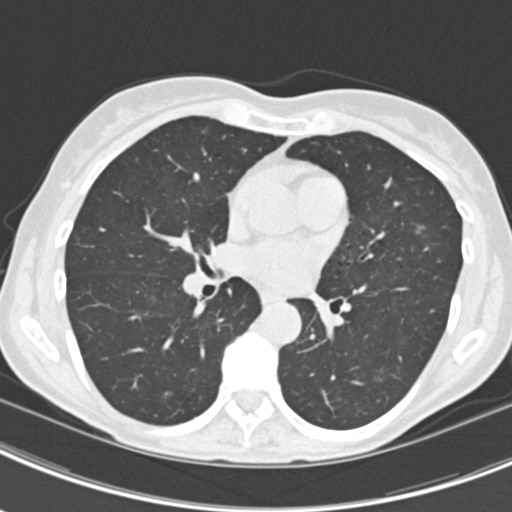
Low-dose screening chest CT, axial slice, second annual screen, lung window (W 1500 / L -600 HU), slice 96 of 219 in the series, 512 × 512 image matrix, field of view 298 × 298 mm. Female participant, aged 63 years at enrolment. Current smoker at enrolment.
Expert-annotated lung lesion, bounding box <401,207,438,254> (left, top, right, bottom; pixels). The screening reader recorded 9 non-calcified nodules or masses ≥4 mm on this exam (left upper lobe, right upper lobe, left upper lobe, left lower lobe, right middle lobe, left lower lobe, left lower lobe, right lower lobe, right lower lobe); which of them this box marks is not recorded. Later outcome: lung cancer diagnosed 408 days after this screen — bronchiolo-alveolar adenocarcinoma, NOS, right upper lobe, right middle lobe, right lower lobe, left upper lobe, left lower lobe, moderately differentiated (G2), stage IV (AJCC 6th edition).